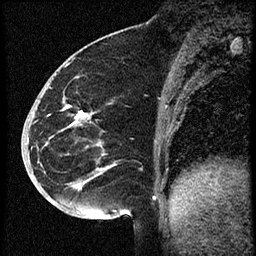
Breast MRI (dynamic contrast-enhanced), one sagittal slice. Position 24 of 60 along the scan axis. Dynamic contrast-enhanced study with each time point stored as its own series, time point 2 of 3 at this slice position (early post-contrast, ordered by acquisition time). 1.5 T. TE 4.2 ms, TR 18.9 ms. 2 mm slice thickness. 256 × 256 image matrix, field of view 200 × 200 mm. Female patient. Case-level facts recorded for this patient, not image findings: setting: breast cancer imaged before/during neoadjuvant chemotherapy; receptor status: HR-positive, HER2-negative.
Outlined on this slice (semi-automatic segmentation, software-assisted and operator-edited):
- analysis volume of interest (the breast-tissue region the enhancement analysis was run in; not a lesion): bounding box [x1, y1, x2, y2] px = [30, 87, 114, 173]
- tumour enhancement mask (voxels above the 100 % enhancement threshold inside the analysis volume of interest): [68, 106, 87, 117]